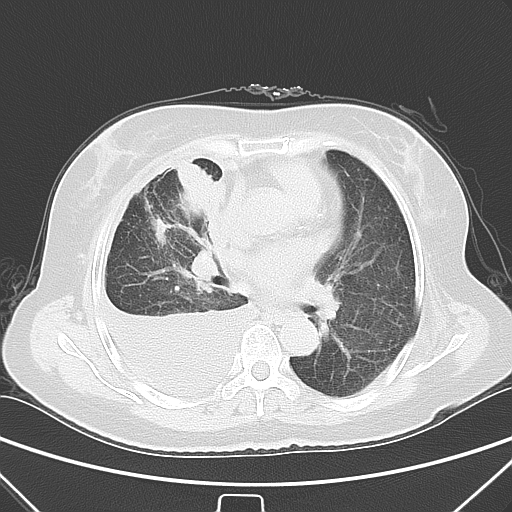
Chest CT, one axial slice; position 33 of 55 along the scan axis; 120 kVp; lung window (W 1500 / L -600 HU); 512 × 512 image matrix, field of view 352 × 352 mm. Female patient, age 66 years. From the clinical record (not read from this slice): clinical TNM (as recorded): T2 N0 M1.
Structures marked on this image (bounding box drawn by a radiologist):
- lung tumour (recorded histology: adenocarcinoma): bounding box [x1, y1, x2, y2] px = [166, 151, 216, 215]